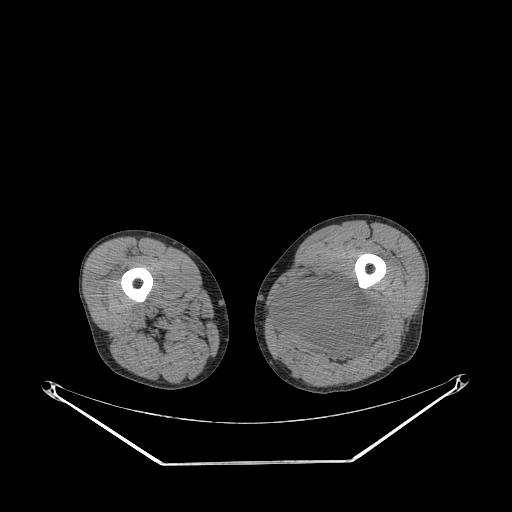
CT of an extremity soft-tissue mass (from a PET/CT study), one axial slice. Slice 232 of 267 in the series (ordered by position). Reconstruction kernel STANDARD. Soft-tissue window (W 400 / L 40 HU). 3.75 mm slice thickness. 512 × 512 image matrix. Male patient. From the clinical record (not read from this slice): histological type: undifferentiated pleomorphic liposarcoma; grade: high; site of the primary tumour: left thigh.
Annotated regions visible in this slice (expert contour drawn on MRI and transferred to this co-registered scan by the dataset authors):
- gross tumour volume including surrounding oedema: bounding box <276,278,380,362> (left, top, right, bottom; pixels)
- gross tumour volume (mass): <276,278,380,360>